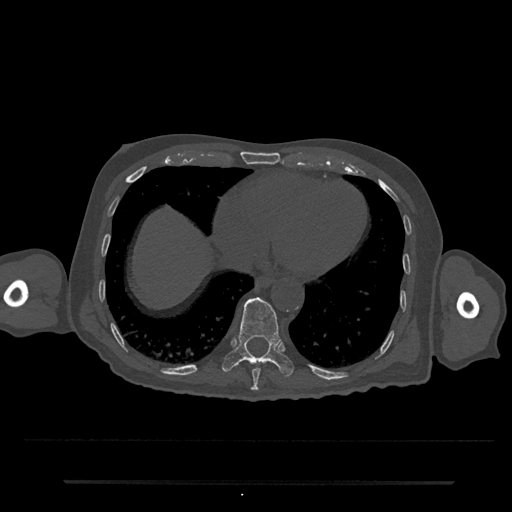
CT including the spine, one axial slice; slice 325 of 797 in the series (ordered by position); 120 kVp; bone window (W 1800 / L 400 HU); 0.5 mm slice thickness; 512 × 512 image matrix, field of view 427 × 427 mm. Male patient, age 74 years. Case-level facts recorded for this patient, not image findings: primary cancer: prostate.
Outlined on this slice (semi-automatic segmentation, software-assisted and operator-edited):
- T10 vertebra: bounding box <222,297,294,377> (left, top, right, bottom; pixels)
- T9 vertebra: <250,363,264,391>